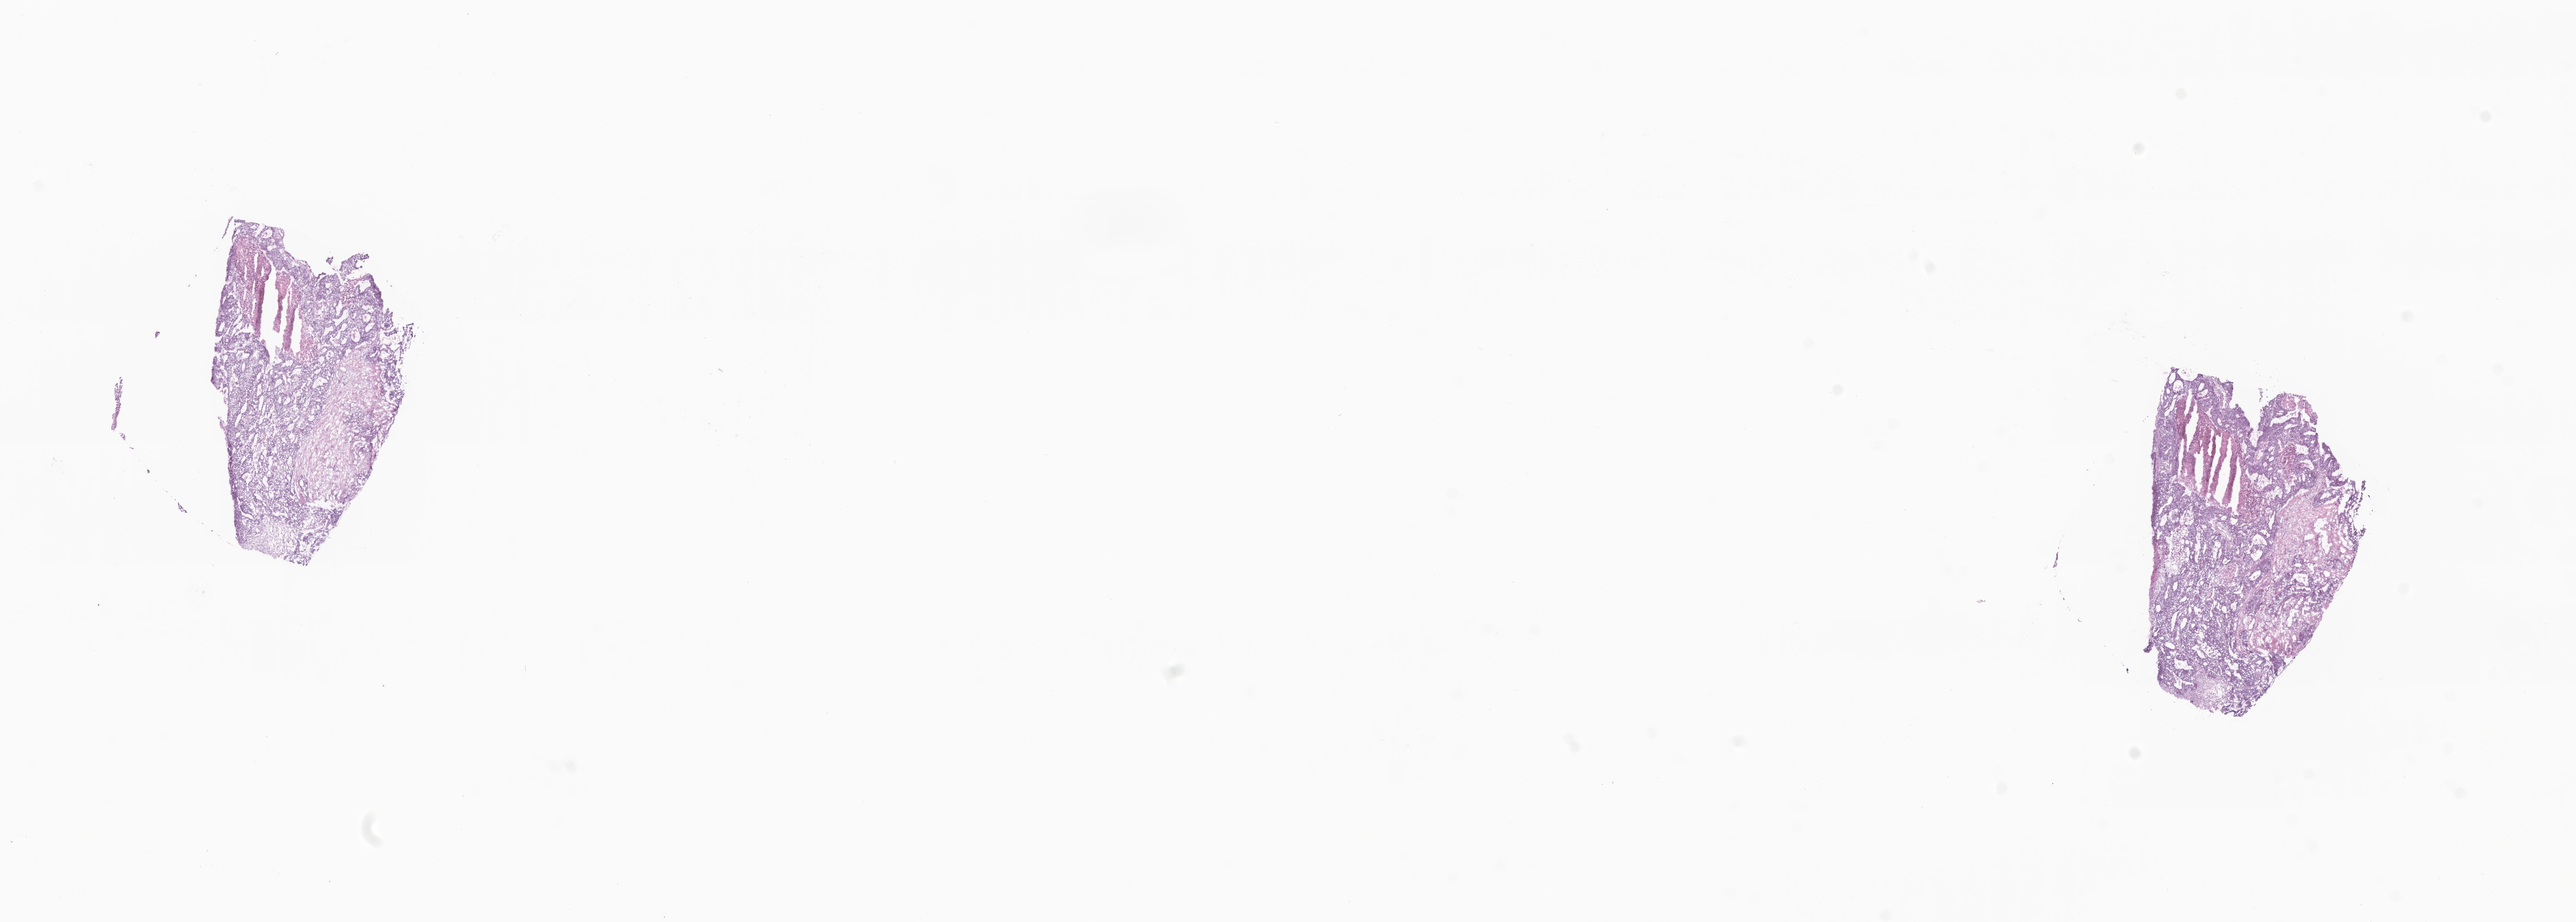
Whole-slide image, H&E stain — a low-resolution overview of the entire scanned area, about 22.6 x 8.1 mm. Frozen section. Specimen: metastatic tumor tissue, resected from liver. Male, age 61 years at initial diagnosis. Slide review estimates, as recorded: tumor cells 80%, tumor nuclei 80%, stromal cells 13%, necrosis 7%, normal cells 0%. Infiltration values recorded for this section: lymphocyte infiltration 4%, monocyte infiltration 1%, neutrophil infiltration 5%.
Patient diagnosis (primary): Adenocarcinoma, NOS.